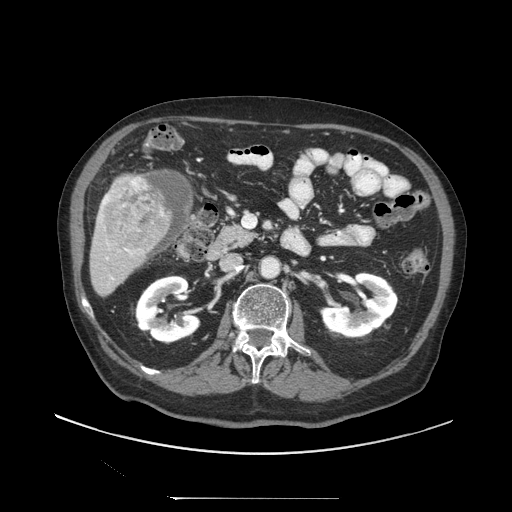
Contrast-enhanced abdominal CT (liver protocol), one axial slice; slice 37 of 97 in the series (ordered by position); reconstruction kernel STANDARD; soft-tissue window (W 400 / L 40 HU); 512 × 512 image matrix, field of view 450 × 450 mm. From the clinical record (not read from this slice): diagnosis: hepatocellular carcinoma (patient treated with transarterial chemoembolisation; whether this scan precedes or follows treatment is not stated here); TNM stage (as recorded): Stage-IIIC; Child-Pugh class: A; tumour nodularity: uninodular; tumour size: 9.2 cm.
Outlined on this slice (semi-automatic segmentation, software-assisted and operator-edited):
- liver parenchyma outside the tumour (the mass and vessels are separate outlines, so this box may not span the whole liver): bounding box <90,174,172,296> (left, top, right, bottom; pixels)
- mass: <104,178,172,250>
- liver vessels: <100,178,140,279>